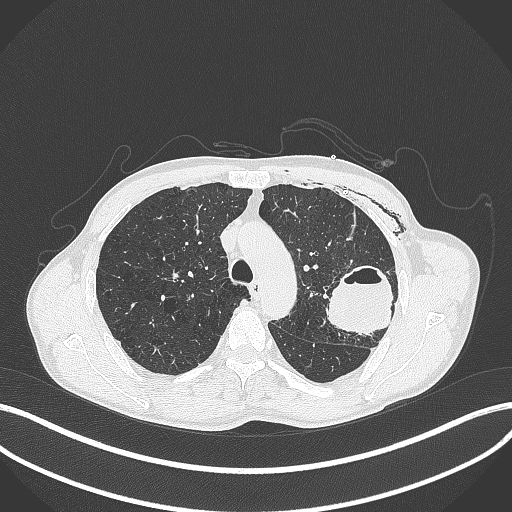
Chest CT, one axial slice. Position 295 of 457 along the scan axis. Reconstruction kernel B70f. 120 kVp. Lung window (W 1500 / L -600 HU). 512 × 512 image matrix, field of view 400 × 400 mm. Patient: male, 58 years. Case-level facts recorded for this patient, not image findings: clinical TNM (as recorded): T3 N0 M0.
Annotated regions visible in this slice (rectangle marked by the reading radiologist):
- lung tumour (recorded histology: adenocarcinoma): bounding box [x1, y1, x2, y2] px = [323, 261, 397, 342]